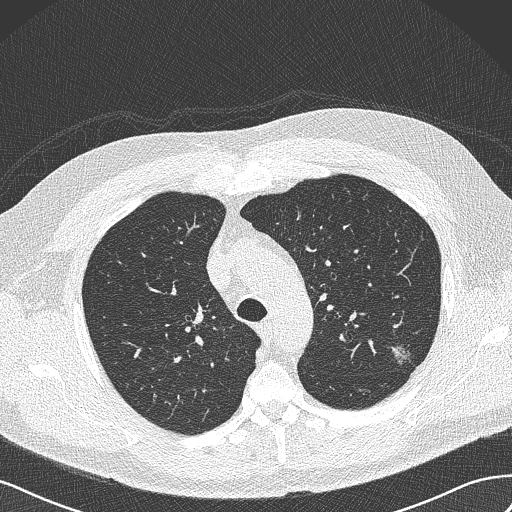
Axial slice from a low-dose chest CT screening exam. Baseline screening round. Lung window (W 1500 / L -600 HU). 512 × 512 image matrix. Male, age 65 years at enrolment.
Expert reader's lesion annotation, bounding box [x1, y1, x2, y2] px = [383, 340, 419, 371]. The screening reader recorded 3 non-calcified nodules or masses ≥4 mm on this exam (left upper lobe, left upper lobe, right upper lobe); which of them this box marks is not recorded. Lung cancer was diagnosed 541 days after this screen (after the second annual screen): adenocarcinoma, NOS, left upper lobe, poorly differentiated (G3), stage IA (AJCC 6th edition), 13 mm at pathology.